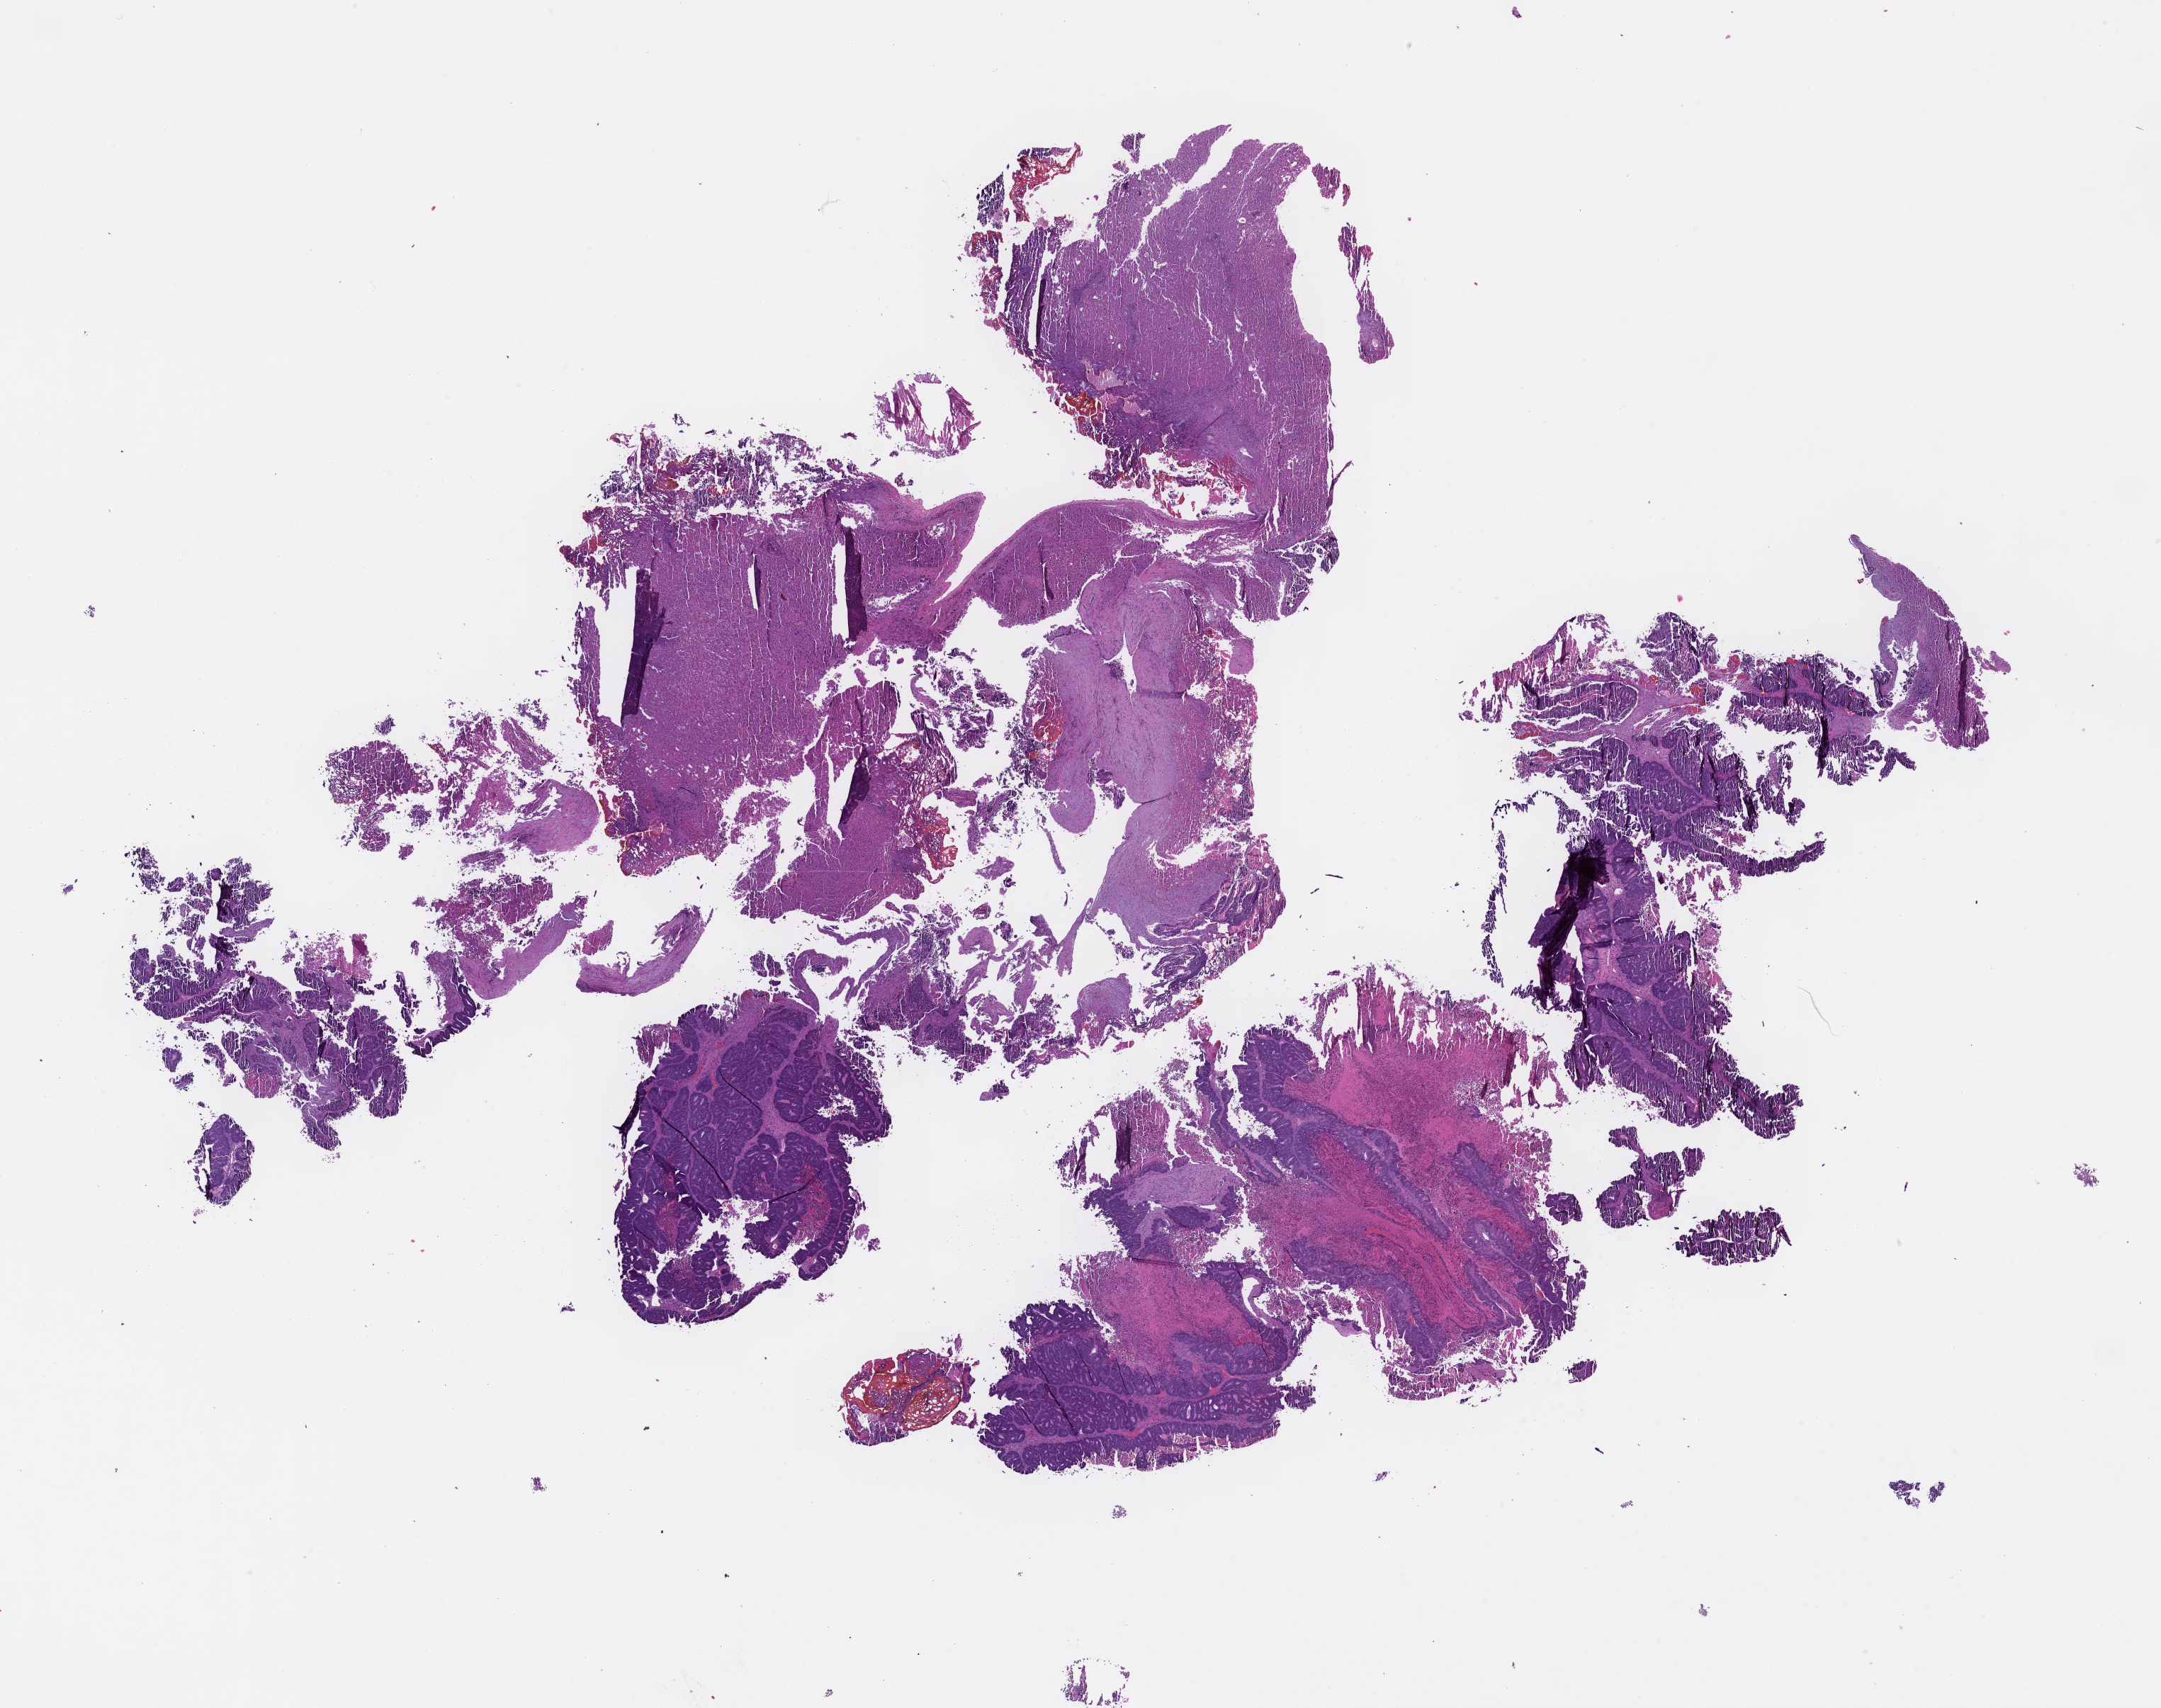
Digitized haematoxylin and eosin-stained section, low-resolution overview of the scanned area, about 24.6 x 19.5 mm. FFPE section. Patient: male.
• this section: metastasis (sampled organ not recorded)
• patient diagnosis (primary): Colorectal Carcinoma